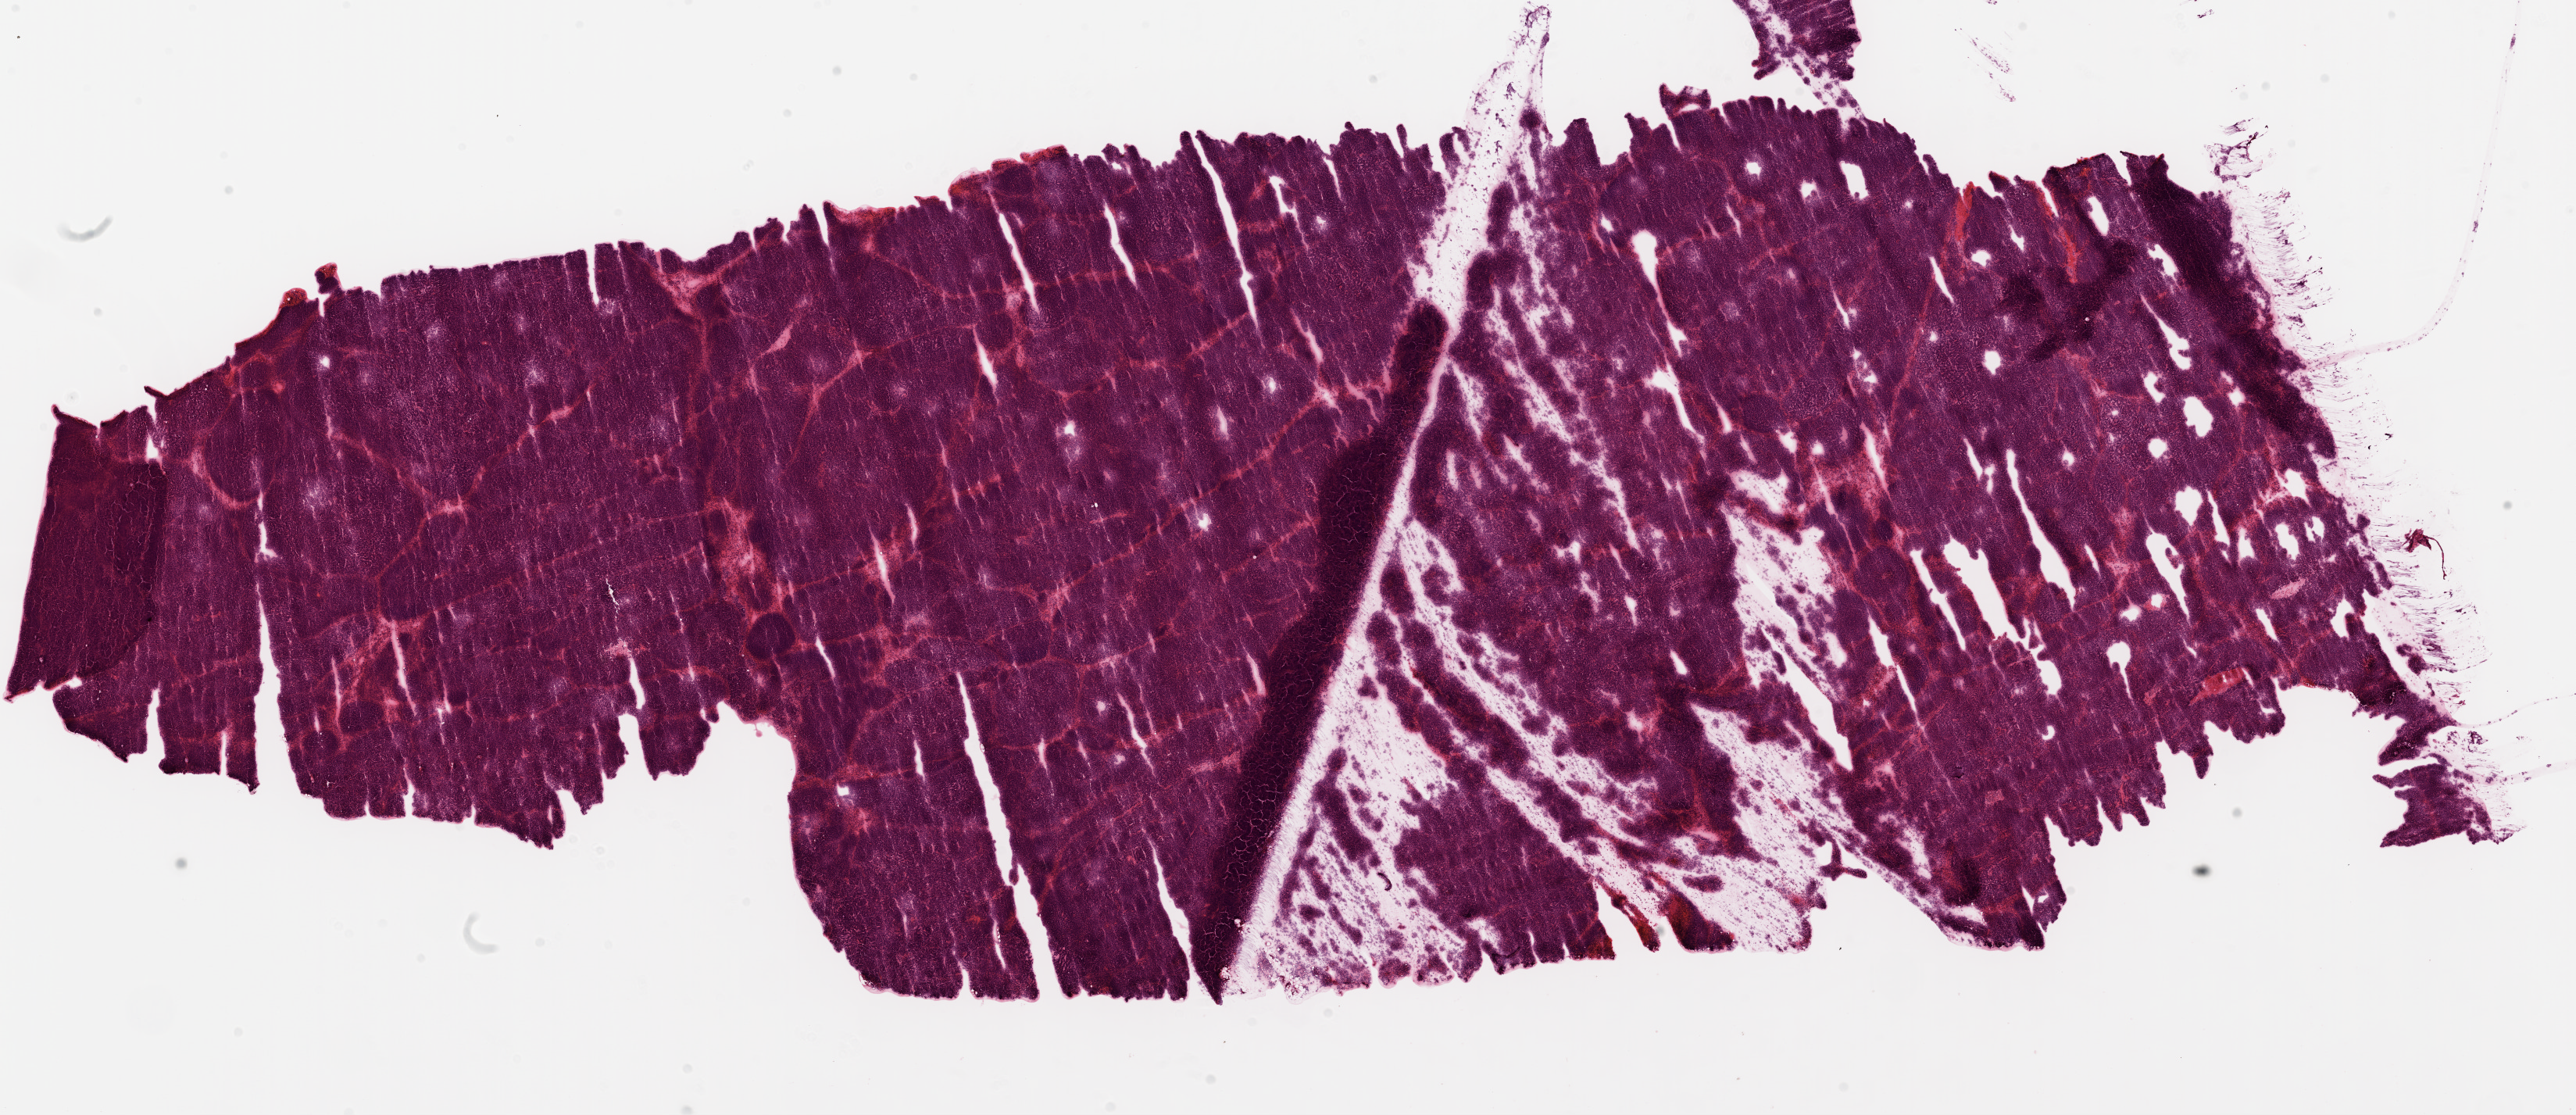
H&E whole-slide image, whole scanned area (about 26.6 x 11.5 mm) shown as a low-resolution overview; frozen section; ovary, primary tumour sample. Patient: female, age at initial diagnosis 55 years. Histologic grade: G3 (poorly differentiated). Slide review estimates, as recorded: tumour cells 98%, tumour nuclei 98%, normal cells 0%, stromal cells 2%, necrosis 0%.
Histologic diagnosis: Serous cystadenocarcinoma, NOS. FIGO stage: IIIC. Laterality: right.